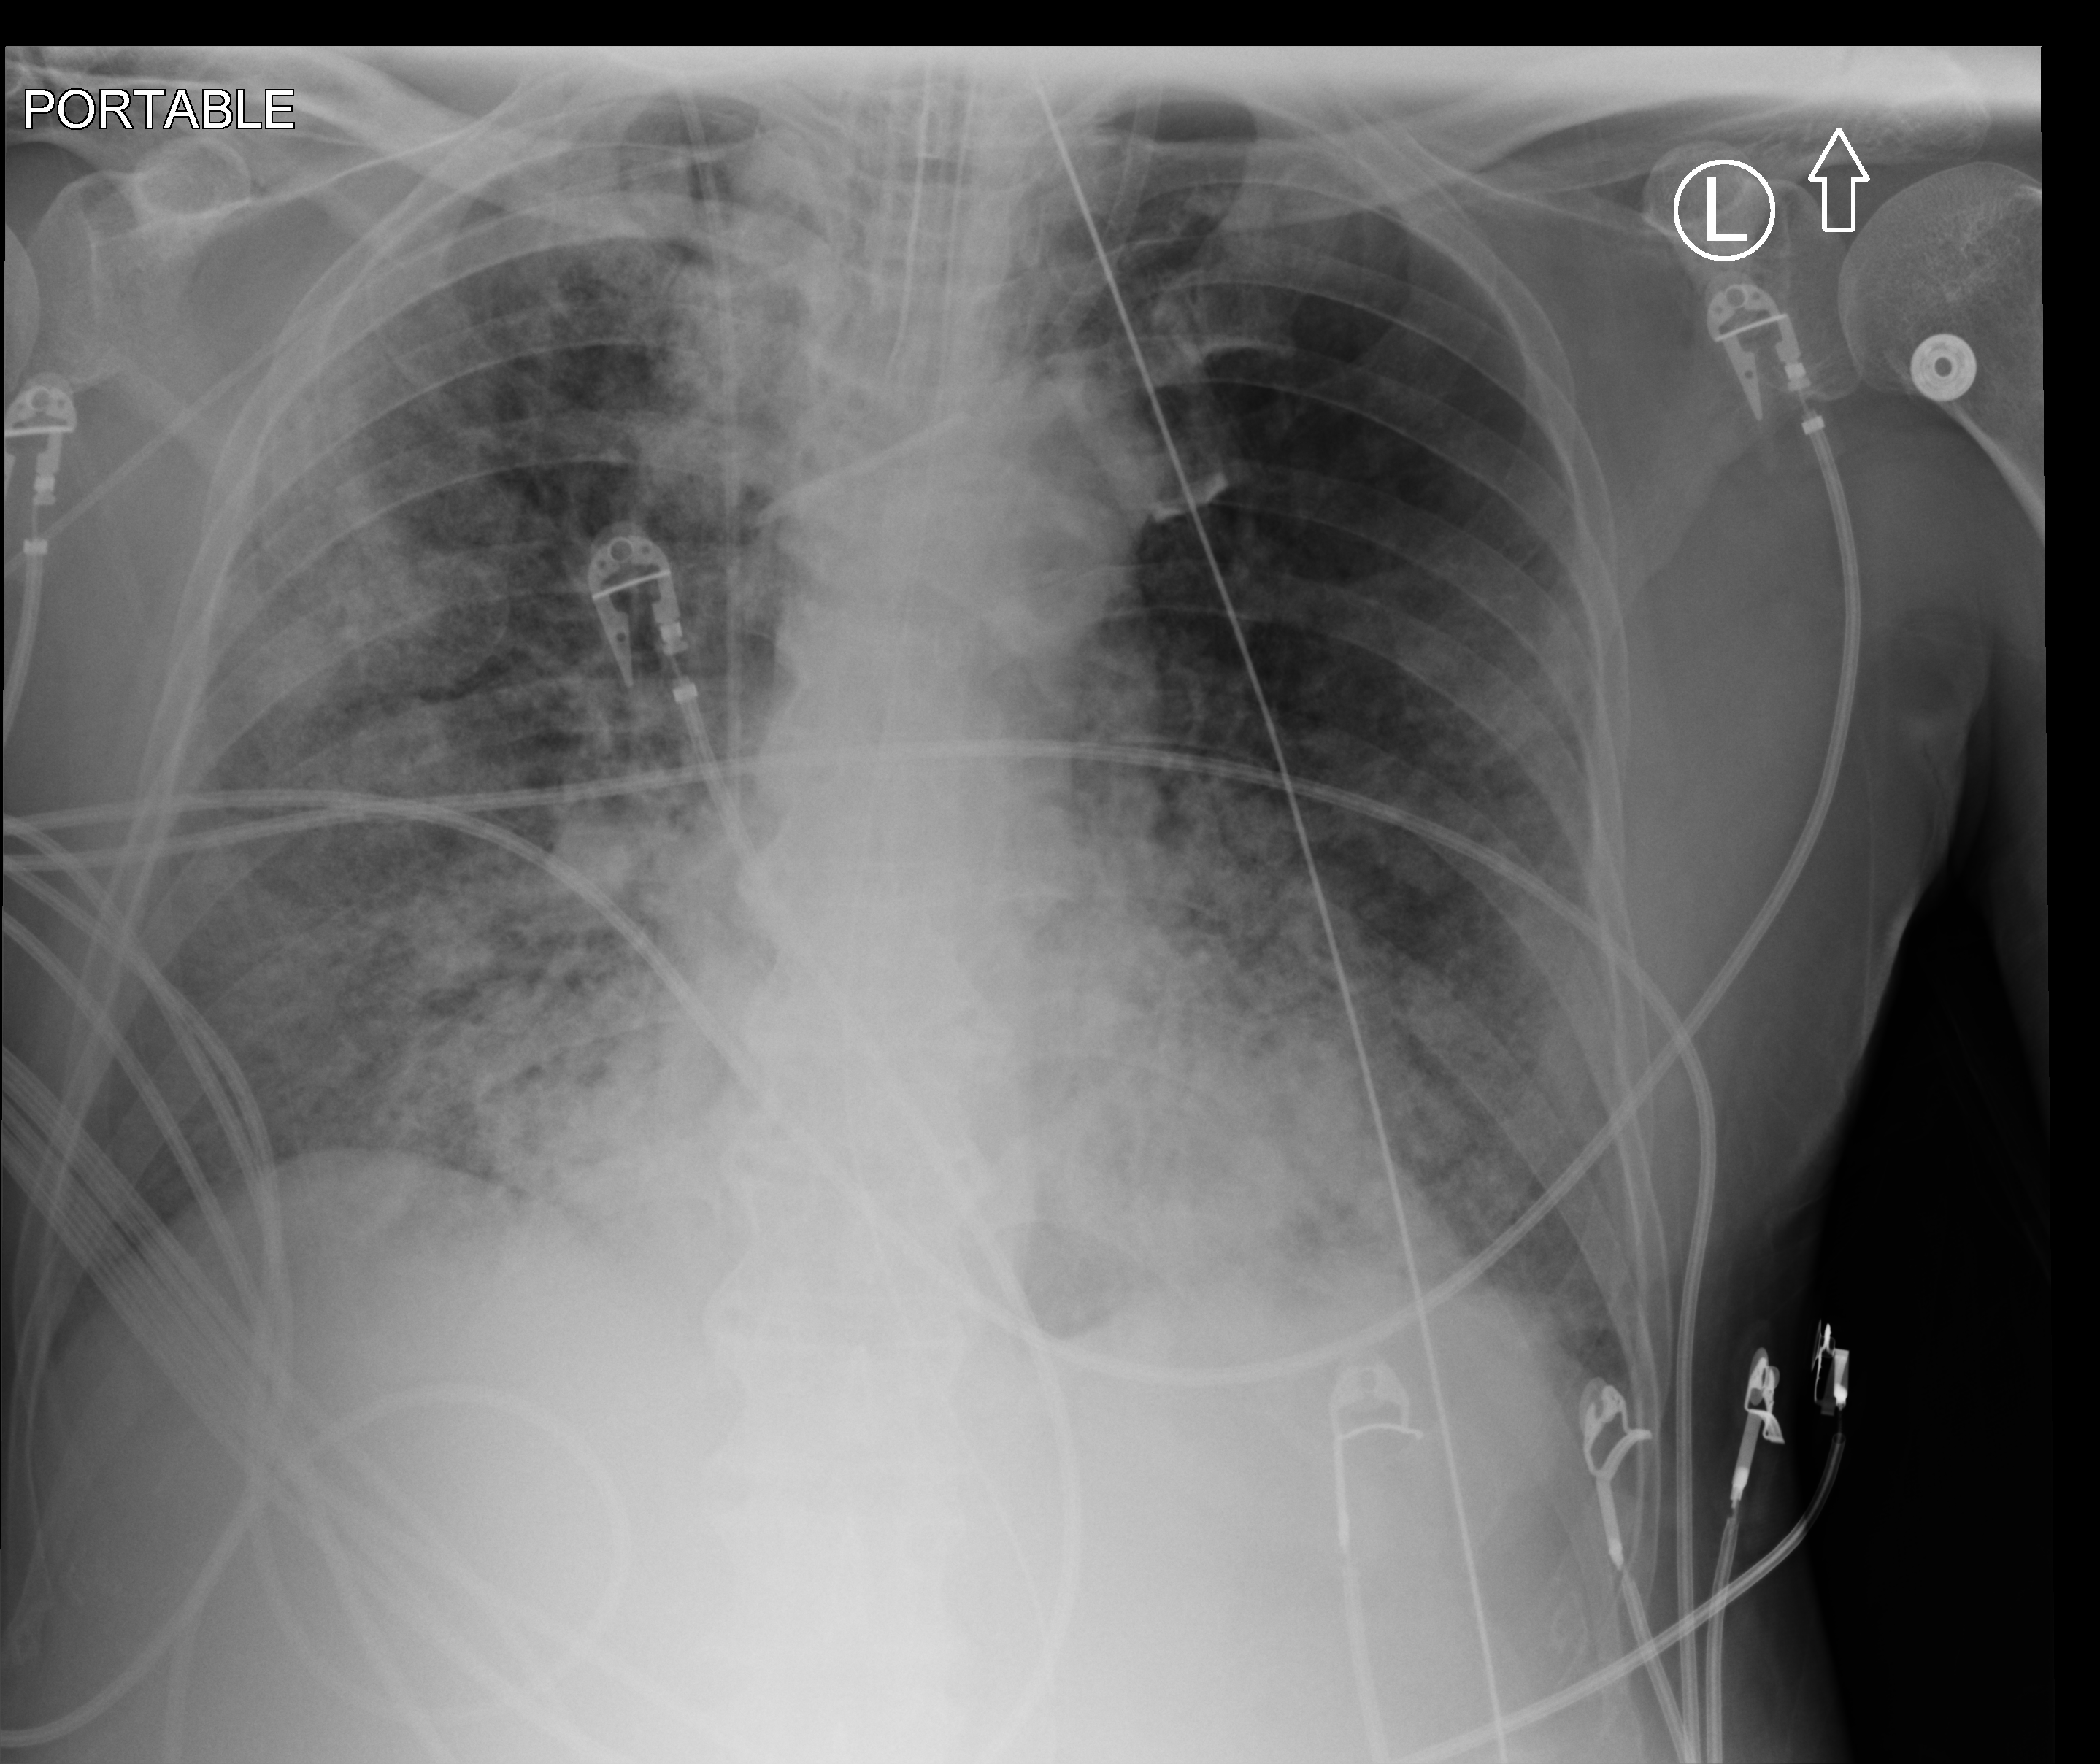
Portable chest radiograph, anteroposterior (AP) projection. Male patient hospitalised with COVID-19, age 60–74 years.
From the hospital-stay record, not from the radiograph (when in the stay this image was taken is not recorded): mechanically ventilated during this hospital stay: yes.